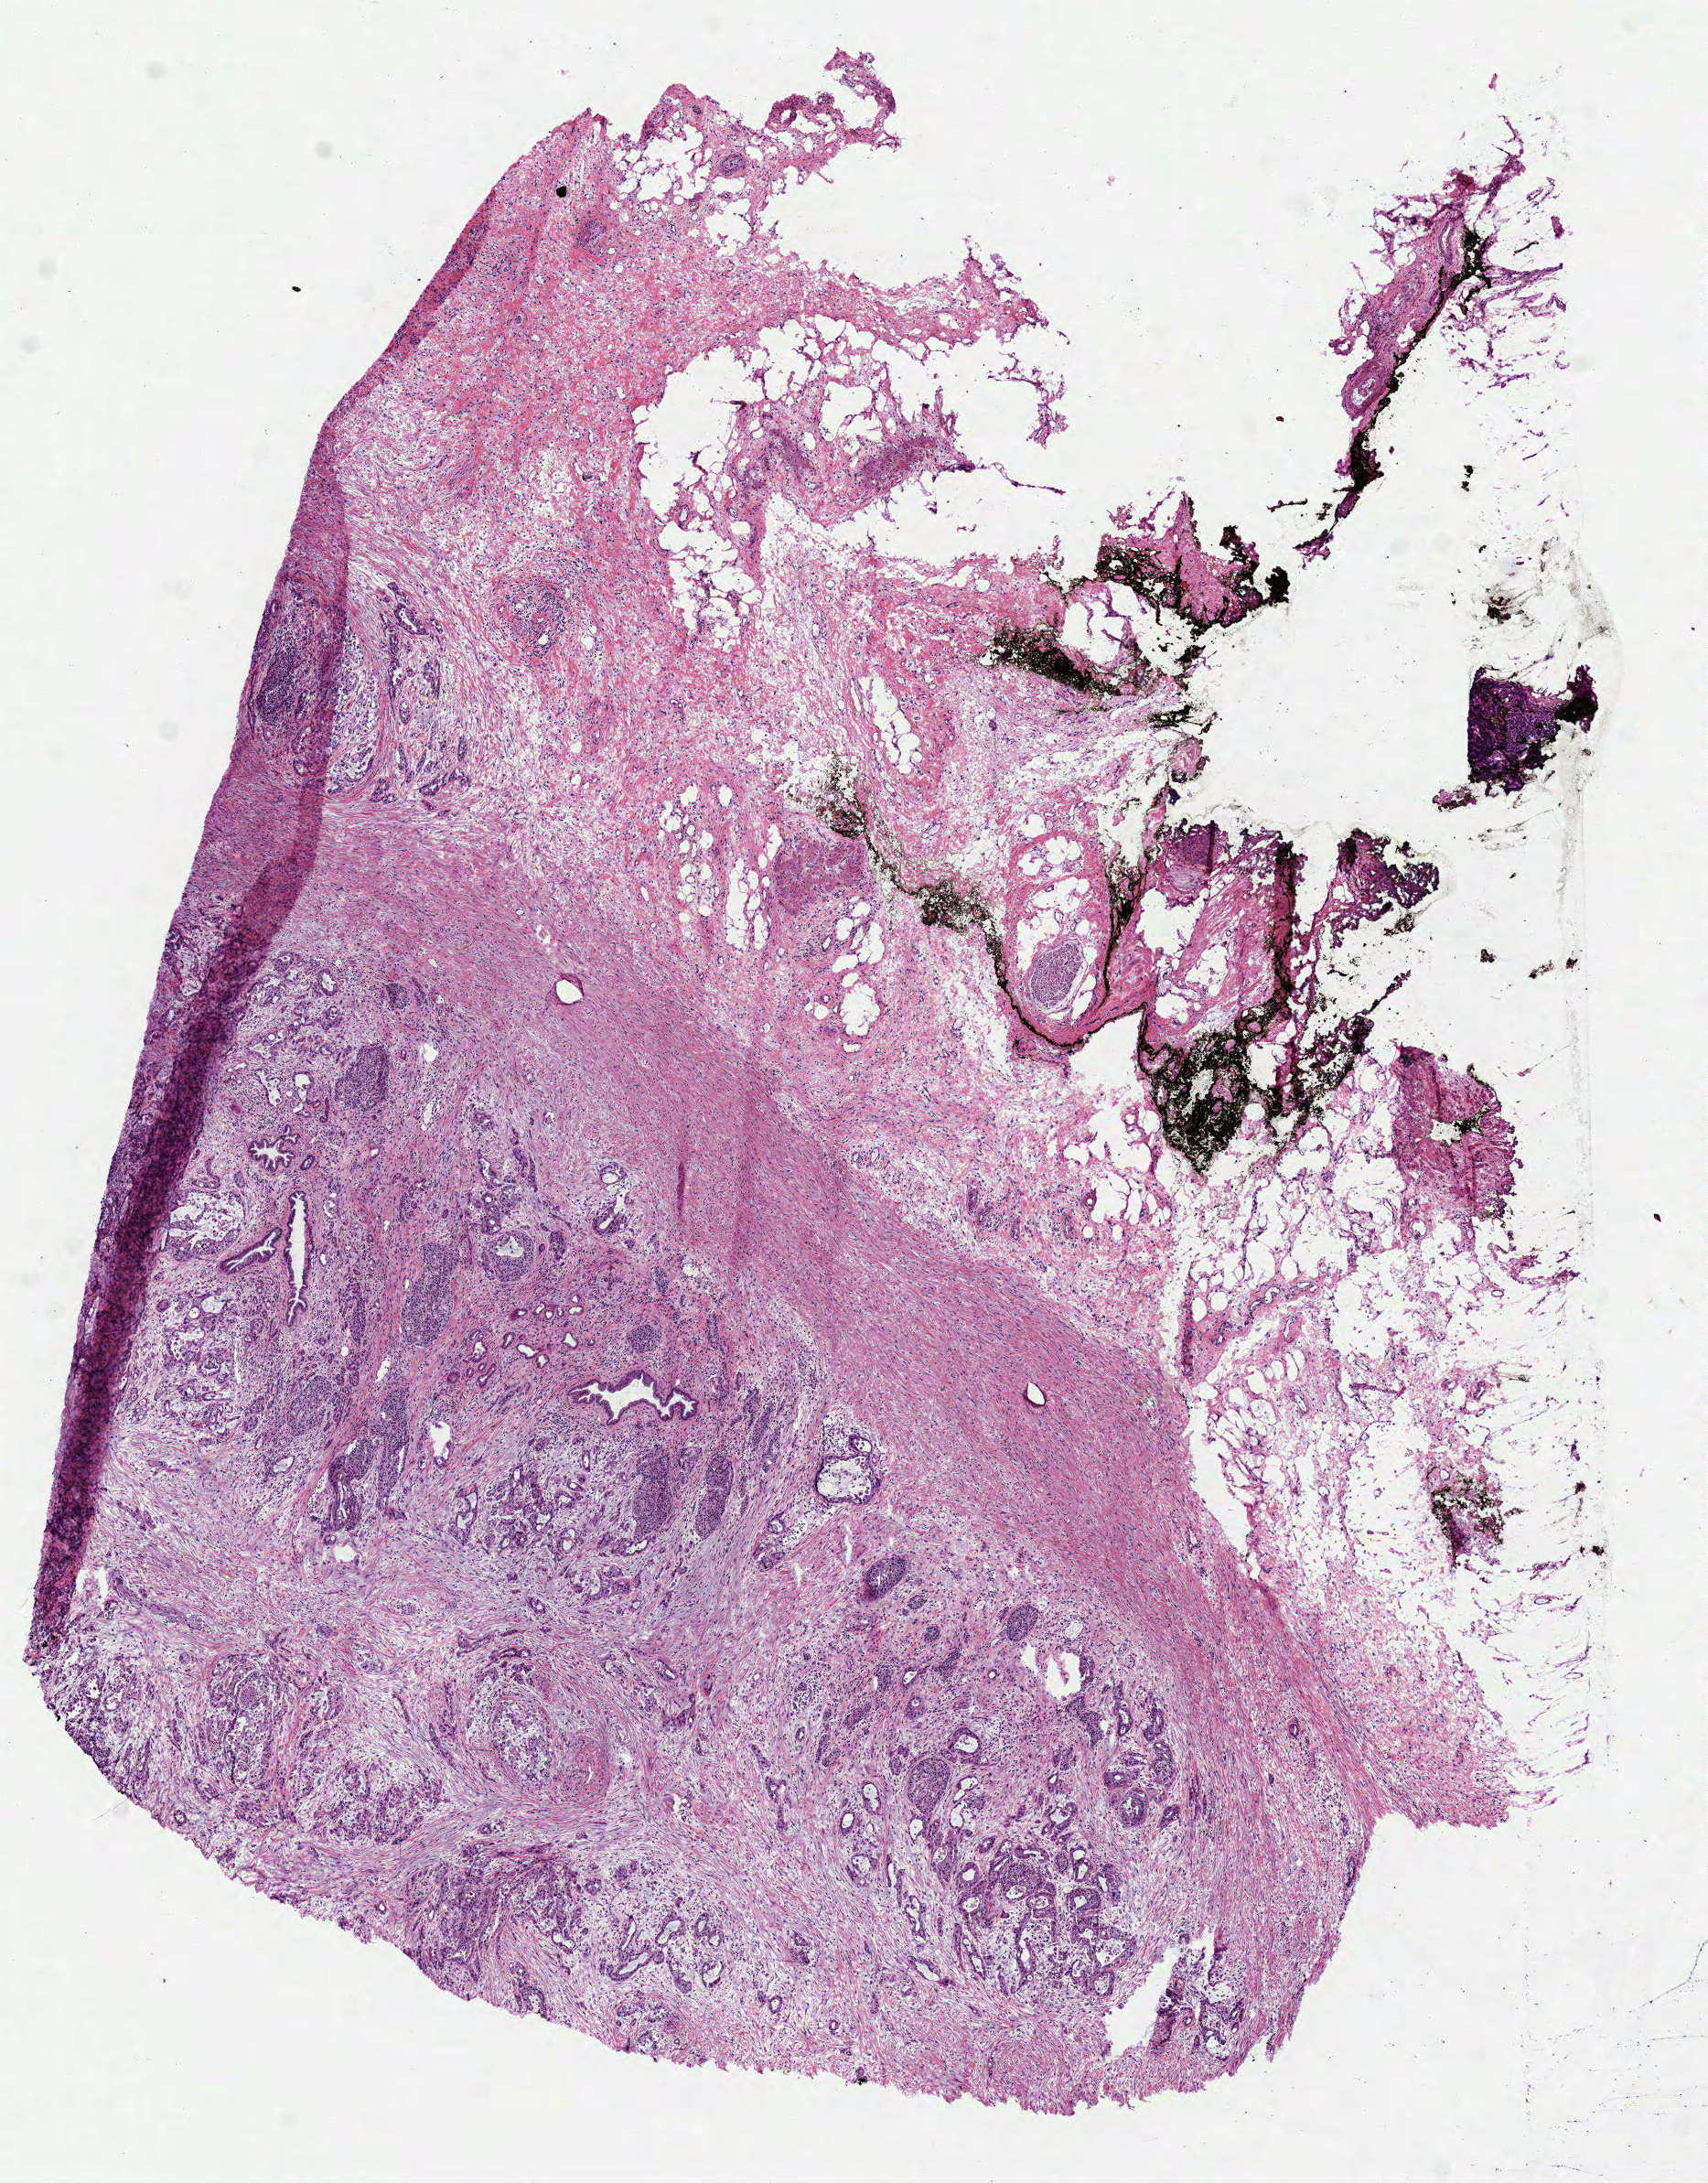
Whole-slide histology image, H&E-stained — a low-resolution overview of the entire scanned area, about 7.5 x 9.6 mm (from a 40x scan). Frozen section from the bottom of the tissue portion. Pancreas, primary tumour sample. Male, age 69 years at initial diagnosis. Histologic grade: G2 (moderately differentiated).
- lymph nodes positive (case pathology): 0 of 16 examined
- histologic diagnosis: Infiltrating duct carcinoma, NOS (head of pancreas)
- AJCC pathologic stage: III (7th edition)